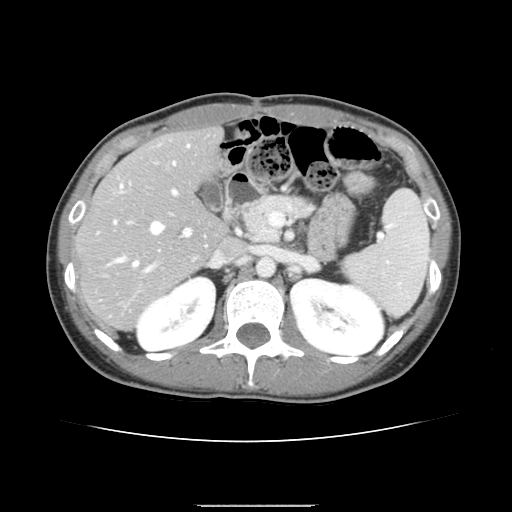
Contrast-enhanced abdominal CT, one axial slice. Slice 86 of 150 in the series (ordered by position). 120 kVp. Intravenous contrast given. Soft-tissue window (W 400 / L 40 HU). 2.5 mm slice thickness. 512 × 512 image matrix, field of view 324 × 324 mm. Female patient, age 32 years. From the clinical record (not read from this slice): diagnosis: colorectal cancer liver metastases, imaged before liver resection; multiple liver metastases: yes; largest metastasis: 0.7 cm; disease in both lobes: no.
Annotated regions visible in this slice (manually delineated by an expert):
- hepatic veins: bounding box <114,145,189,266> (left, top, right, bottom; pixels)
- liver: <78,129,227,330>
- planned liver remnant (the part of the liver to remain after resection): <78,129,226,276>
- portal vein (with intrahepatic branches): <109,188,191,271>